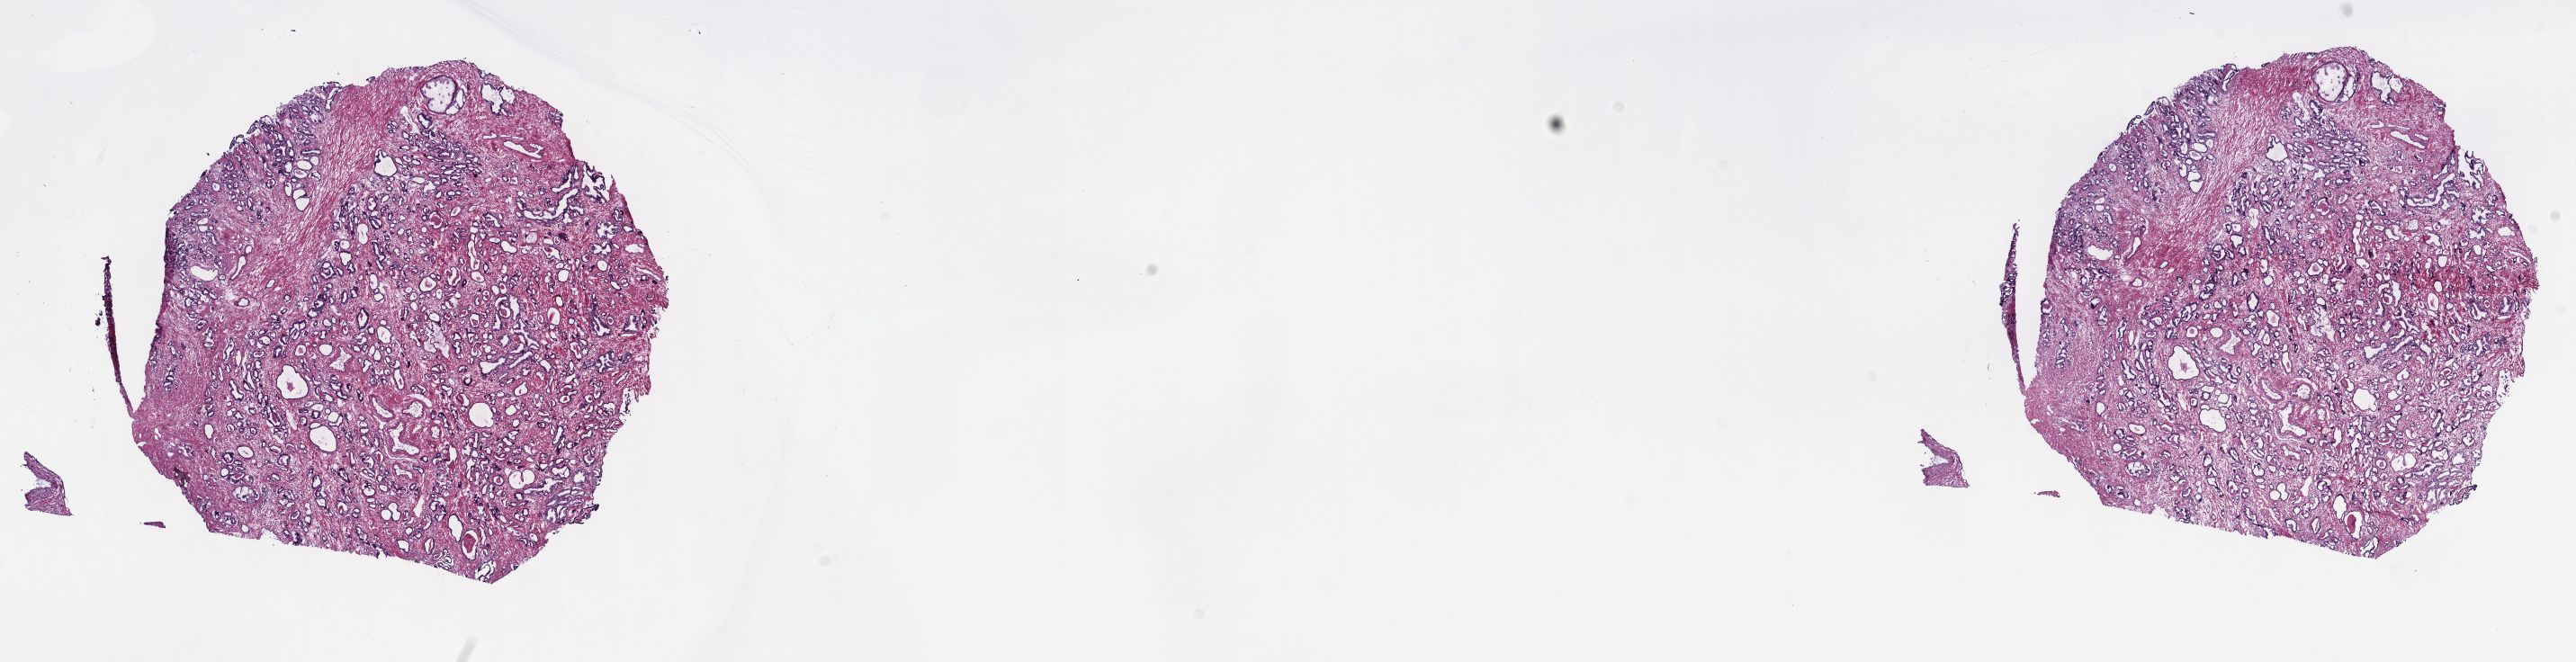
H&E-stained whole-slide image, shown as a low-resolution overview of the whole scanned area (about 23.2 x 6.0 mm, slide scanned at 40x), frozen section from the top of the tissue portion, primary tumour sample from the prostate. Male, age 52 years at initial diagnosis. Gleason score: 6 (3+3). Slide review estimates, as recorded: tumour cells 45%, tumour nuclei 80%, normal cells 7%, stromal cells 45%, necrosis 3%. Inflammatory infiltration, as recorded: lymphocyte infiltration 4%, monocyte infiltration 1%, neutrophil infiltration 1%.
Diagnosis: Adenocarcinoma, NOS (prostate gland). Lymph nodes positive (case pathology): 0 of 16 examined.